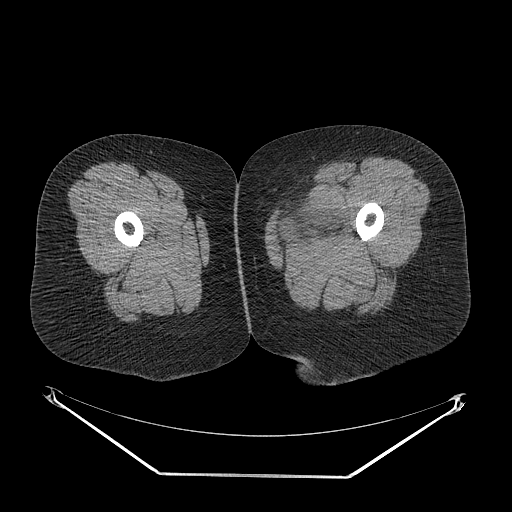
CT of an extremity soft-tissue mass (from a PET/CT study), one axial slice; position 15 of 267 along the scan axis; reconstruction kernel STANDARD; soft-tissue window (W 400 / L 40 HU); 512 × 512 image matrix, field of view 500 × 500 mm. Female patient. Case-level facts recorded for this patient, not image findings: histological type: myxofibrosarcoma; grade: intermediate; site of the primary tumour: left thigh.
Outlined on this slice (expert contour drawn on MRI and transferred to this co-registered scan by the dataset authors):
- gross tumour volume including surrounding oedema: box from (x=278, y=199) to (x=353, y=245) px
- gross tumour volume (mass): (x=294, y=199)–(x=339, y=225)